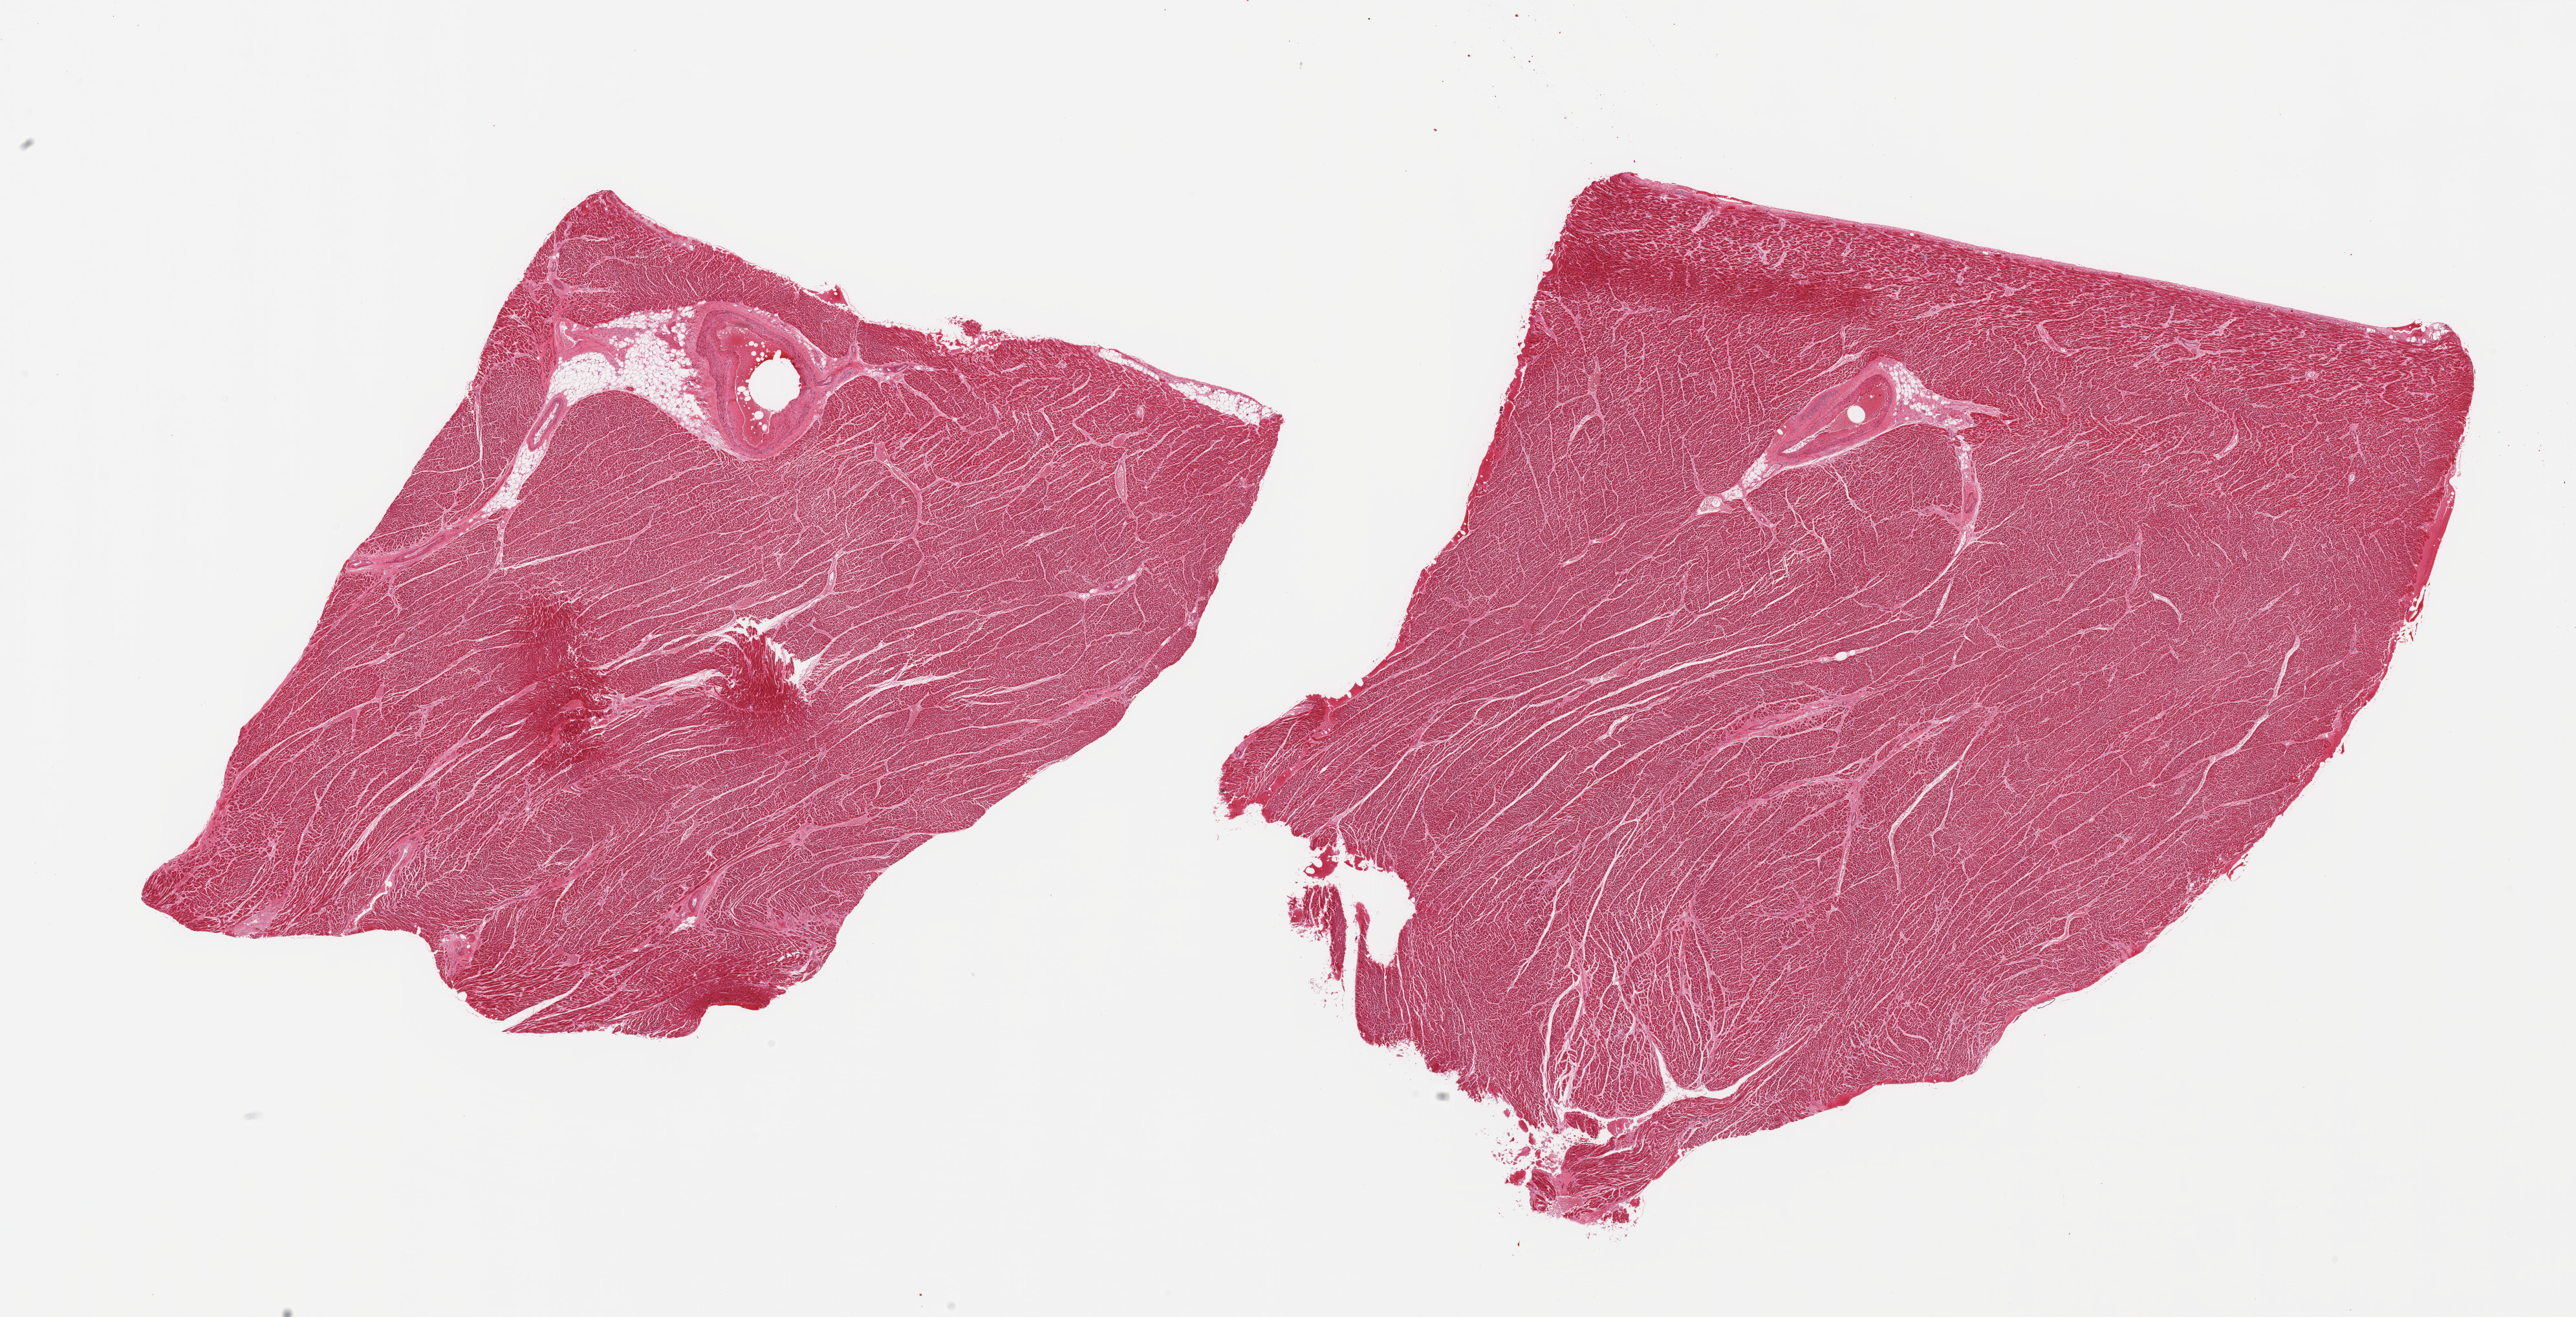
Whole-slide image, haematoxylin and eosin stain — low-resolution overview of the scanned area, about 31.5 x 16.1 mm (slide scanned at 20x). PAXgene-fixed paraffin-embedded (PFPE) section. Sampled site (target tissue): heart. Tissue donor sample.
• reviewer comment on this tissue sample: 2 pieces; perivascular fatty accumulation; patchy increased eosinophilia and fragmentation of fibers suggestive of early acute myocardial infarction; interstitial fibrosis with scarring